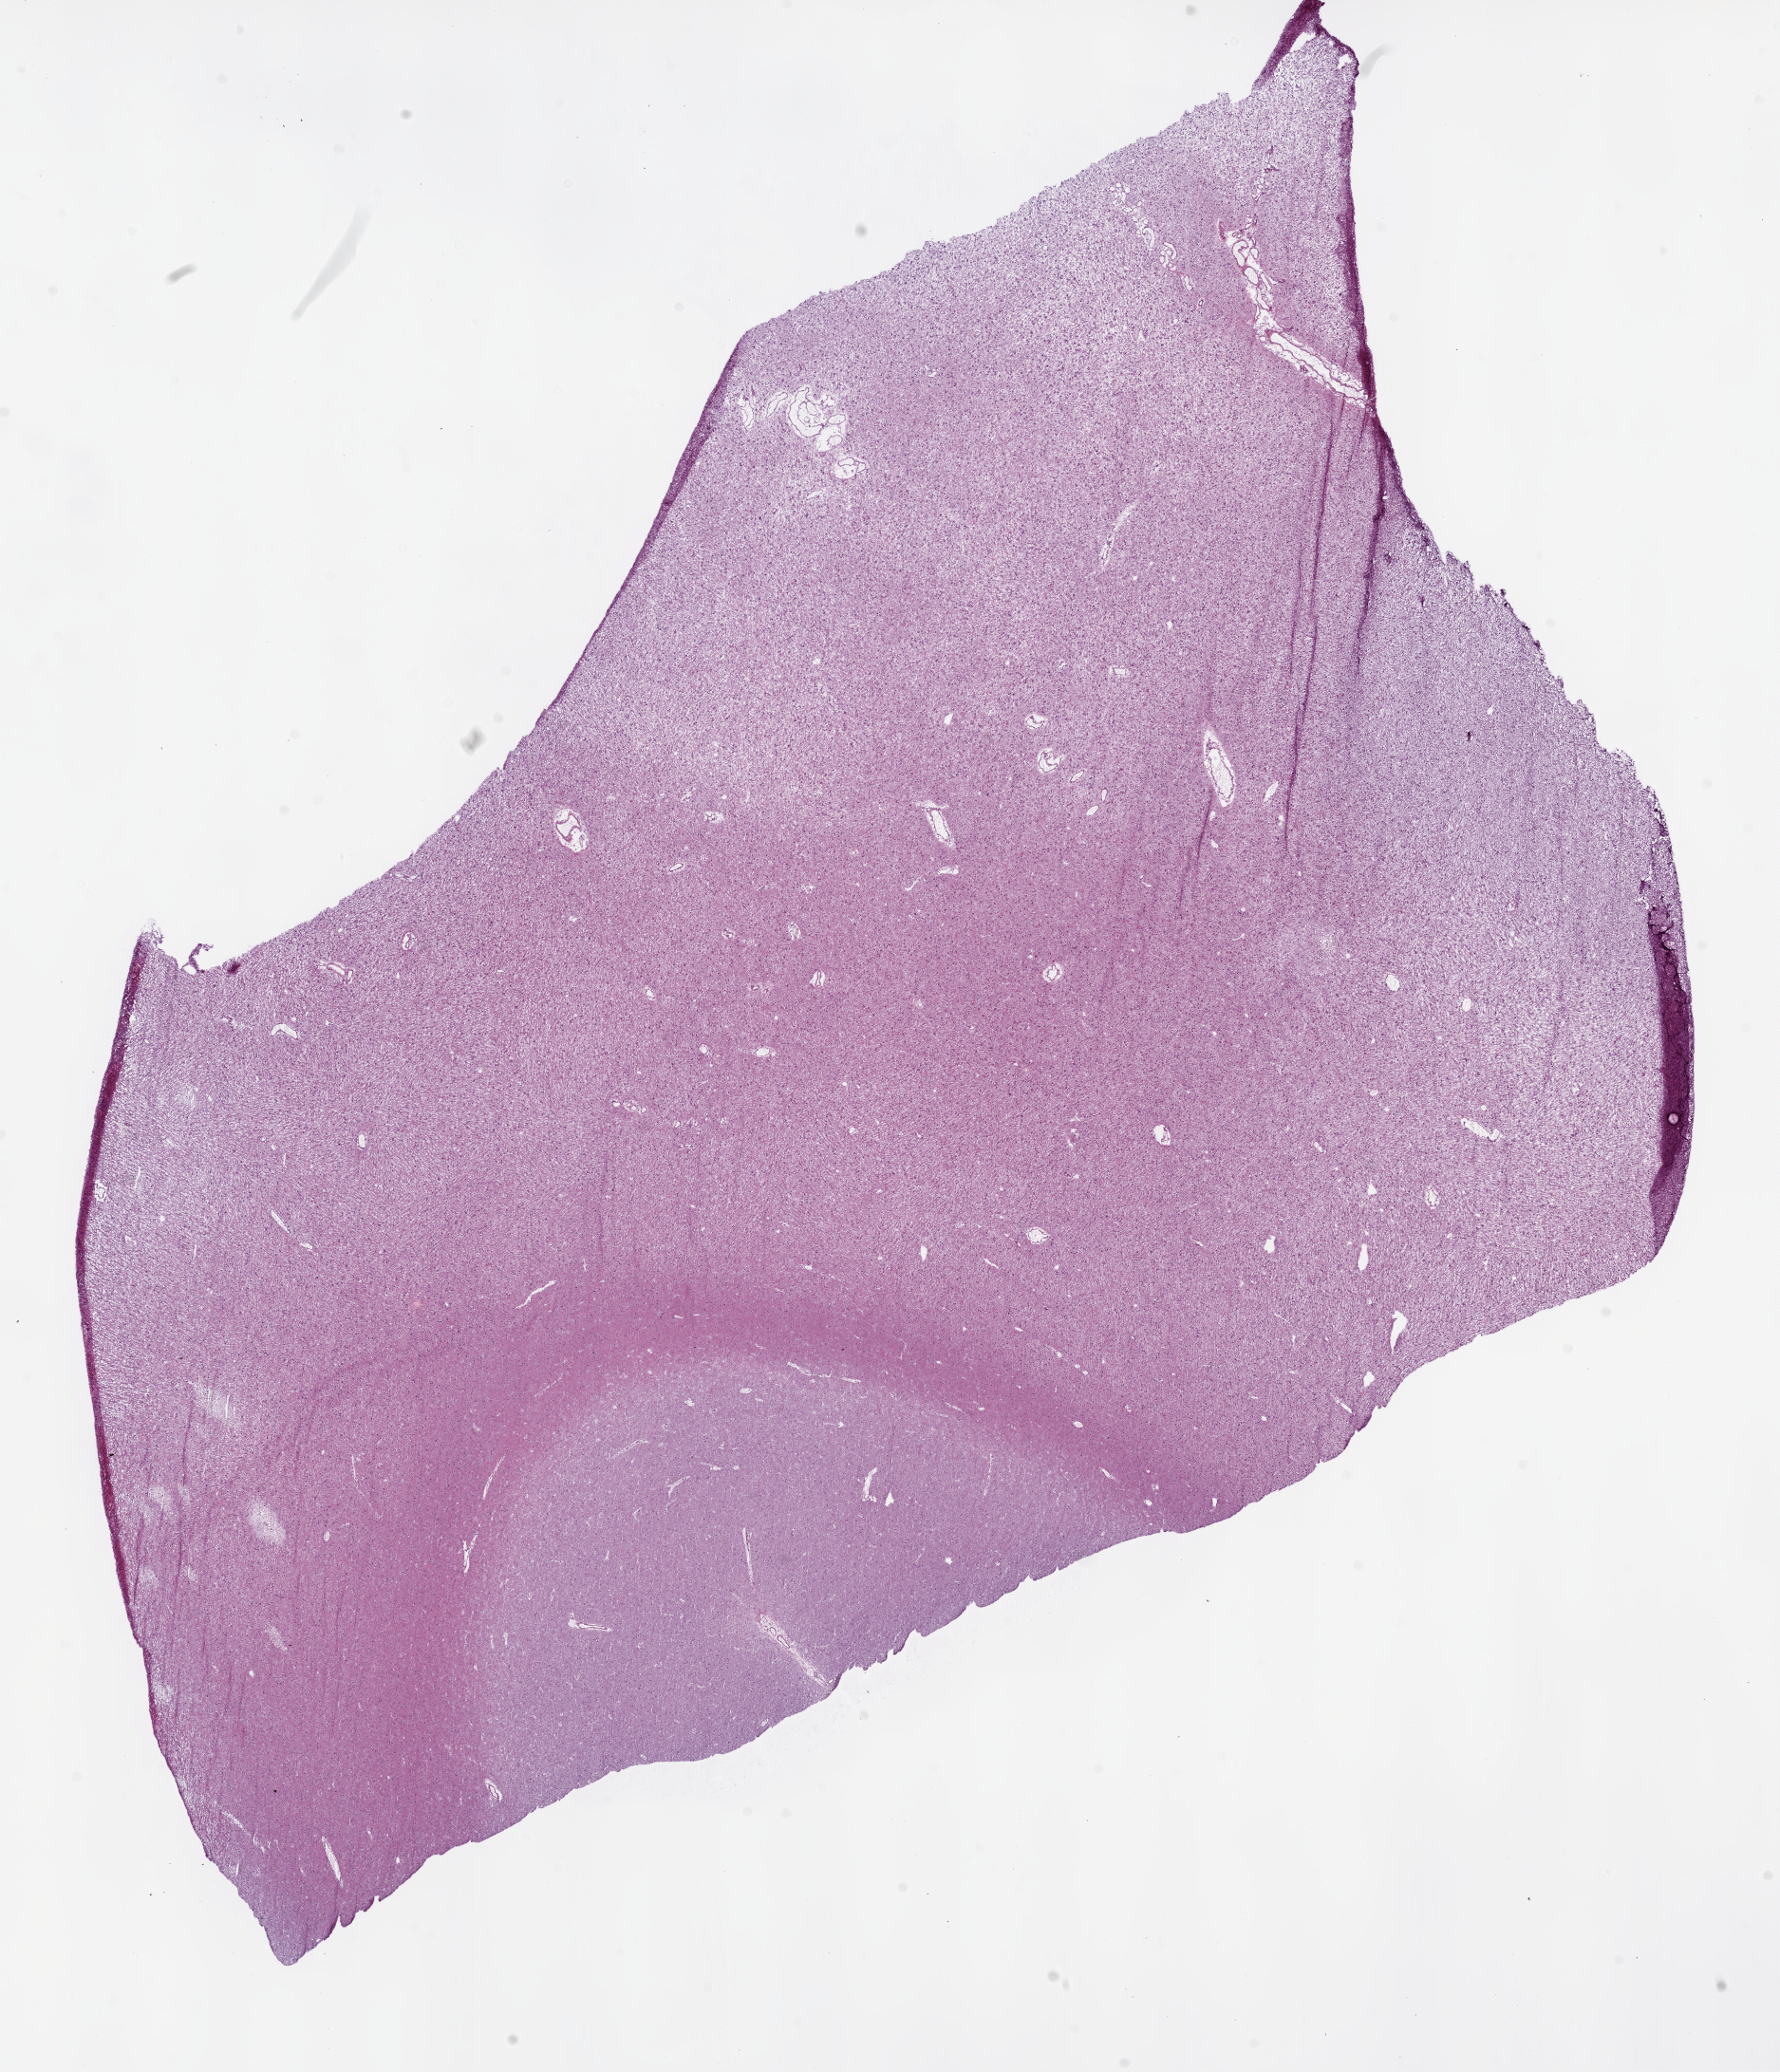
H&E whole-slide image — a low-resolution overview of the entire scanned area, about 15.0 x 17.5 mm (from a 20x scan); frozen section from the bottom of the tissue portion; sample: primary tumour, brain. Patient: male, age at initial diagnosis 32 years. Histologic grade: G3 (poorly differentiated). Pathologist review of this section (percent, as recorded): tumour cells 100%, tumour nuclei 60%, normal cells 0%, stromal cells 0%, necrosis 0%.
• diagnosis: Mixed glioma